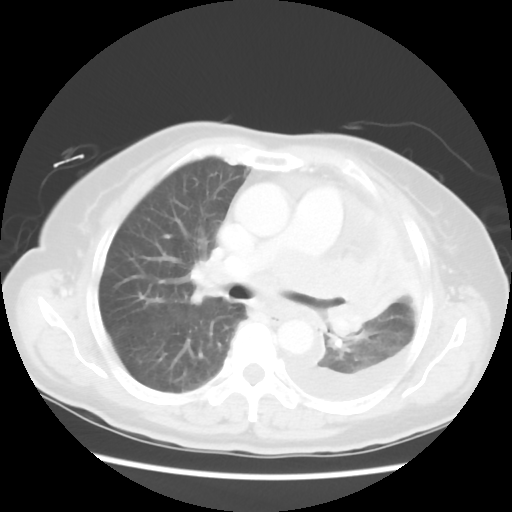
Chest CT, one axial slice; slice 33 of 52 in the series (ordered by position); 120 kVp; lung window (W 1500 / L -600 HU); 5 mm slice thickness; 512 × 512 image matrix, field of view 336 × 336 mm. Patient: female, 72 years. From the clinical record (not read from this slice): clinical TNM (as recorded): T4 N3 M1b.
Outlined on this slice (bounding box drawn by a radiologist):
- lung tumour (recorded histology: large cell carcinoma): bounding box (x1, y1, x2, y2) in pixels: (312, 248, 391, 342)